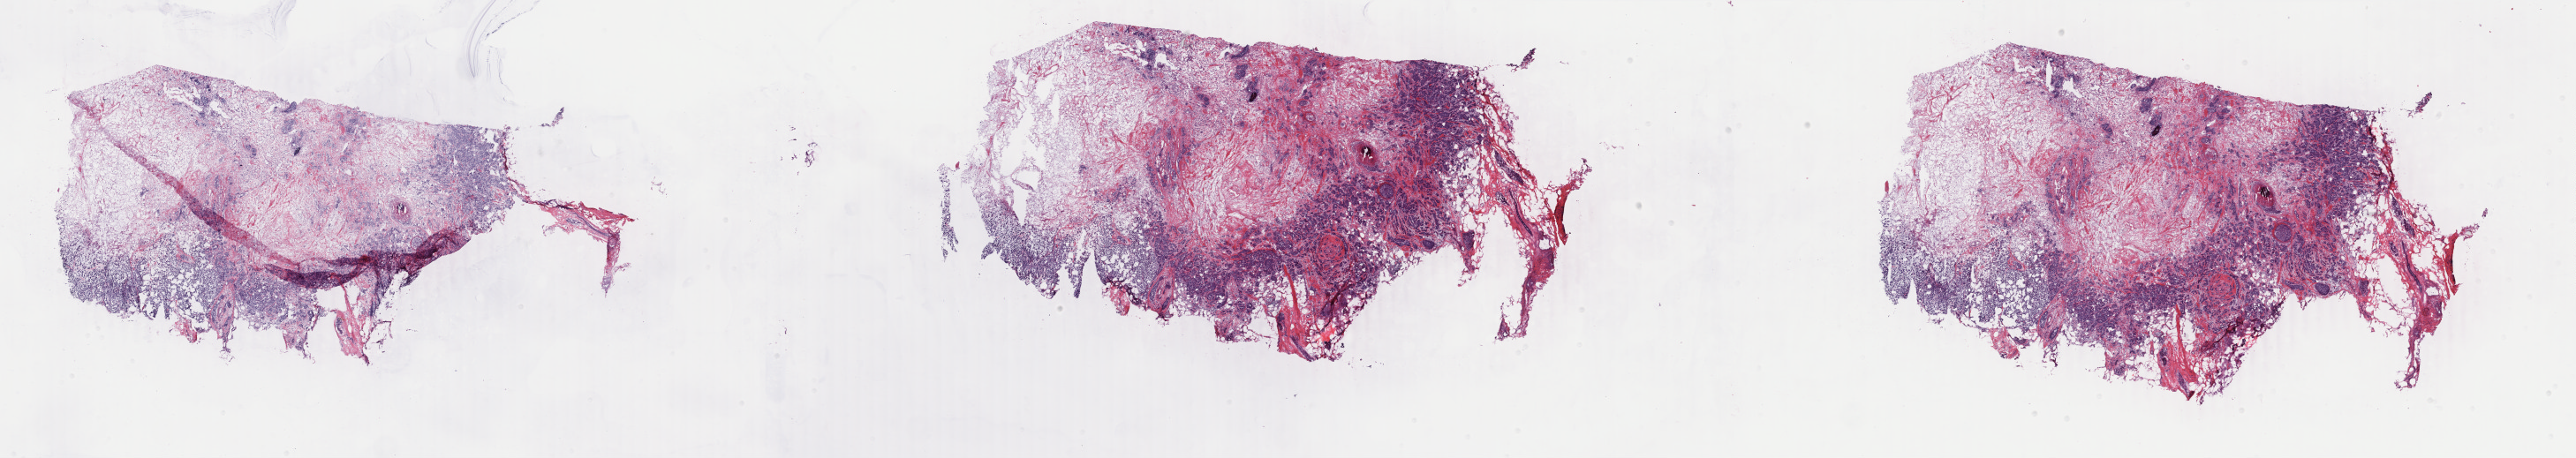
Digitized H&E-stained tissue section (whole slide) — shown as a low-resolution overview of the whole scanned area (about 46.4 x 8.3 mm). Frozen section. Sample: primary tumour, breast. Patient: female, age at initial diagnosis 52 years. Pathologist review of this section (percent, as recorded): tumour cells 40%, tumour nuclei 80%, normal cells 8%, stromal cells 32%, necrosis 20%. Inflammatory infiltration, as recorded: lymphocyte infiltration 2%, monocyte infiltration 3%, neutrophil infiltration 0%.
AJCC pathologic stage: IIA. Lymph nodes positive (case pathology): 0 of 12 examined. Histologic diagnosis: Infiltrating duct carcinoma, NOS. Laterality: left.